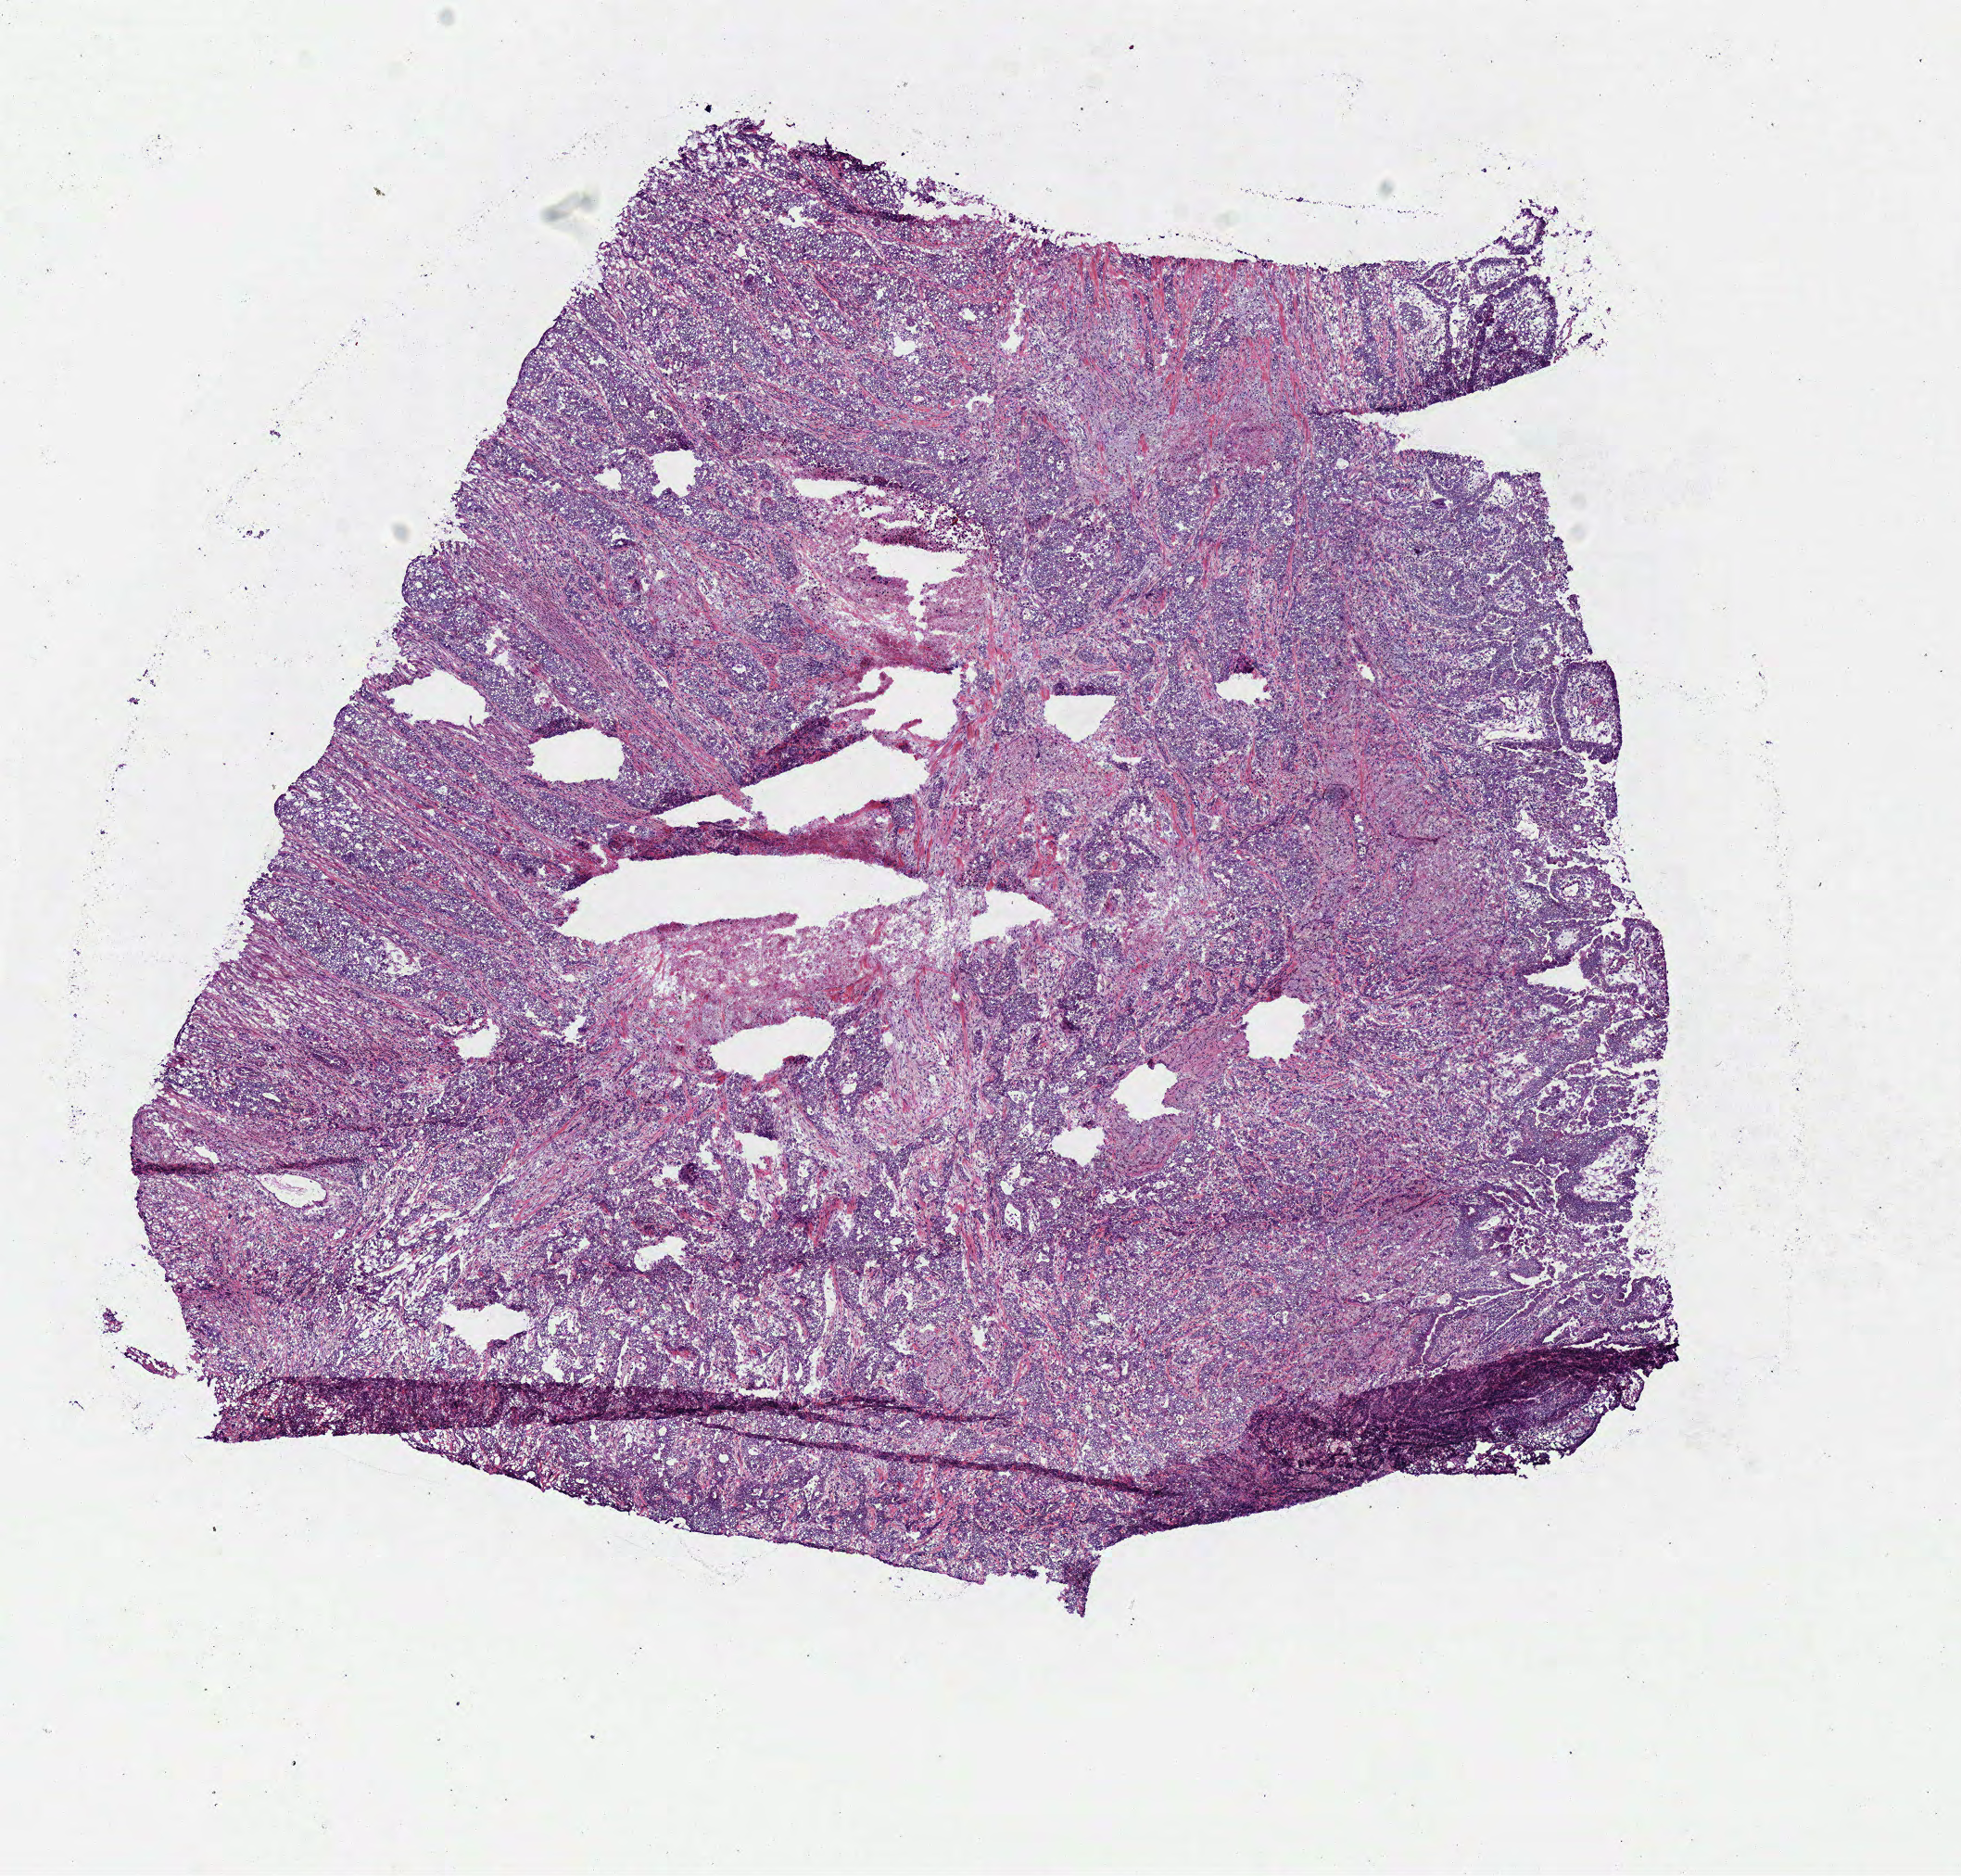
H&E-stained whole-slide image — a low-resolution overview of the entire scanned area, about 8.3 x 8.0 mm (slide scanned at 40x). Frozen section from the bottom of the tissue portion. Stomach, primary tumour sample. Male, age 58 years at initial diagnosis. Histologic grade: G3 (poorly differentiated). Pathologist review of this section (percent, as recorded): tumour cells 70%, tumour nuclei 75%, normal cells 0%, stromal cells 20%, necrosis 10%.
Lymph nodes positive (case pathology): 6 of 9 examined. Histologic diagnosis: Carcinoma, diffuse type (cardia, NOS). TNM: T2 N2 M0. AJCC pathologic stage: IIIA (6th edition).